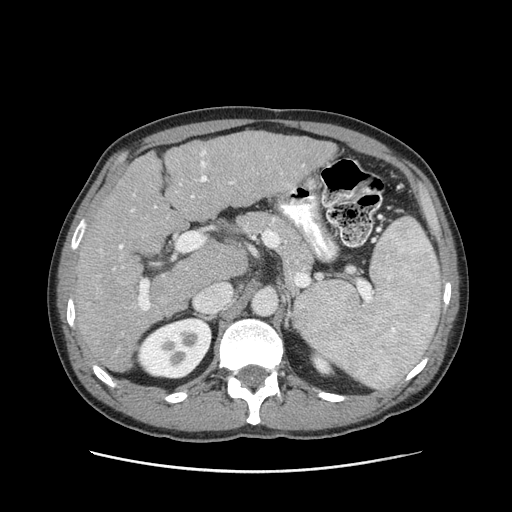
Contrast-enhanced abdominal CT (liver protocol), one axial slice. Position 55 of 93 along the scan axis. Reconstruction kernel STANDARD. 120 kVp. Soft-tissue window (W 400 / L 40 HU). 2.5 mm slice thickness. 512 × 512 image matrix. Case-level facts recorded for this patient, not image findings: diagnosis: hepatocellular carcinoma (patient treated with transarterial chemoembolisation; whether this scan precedes or follows treatment is not stated here); TNM stage (as recorded): Stage-II; Child-Pugh class: A; tumour differentiation: moderately differentiated; tumour nodularity: multinodular.
Outlined on this slice (semi-automatically segmented with operator editing):
- liver parenchyma outside the tumour (the mass and vessels are separate outlines, so this box may not span the whole liver): bounding box [x1, y1, x2, y2] px = [76, 130, 336, 372]
- liver vessels: [100, 150, 304, 311]